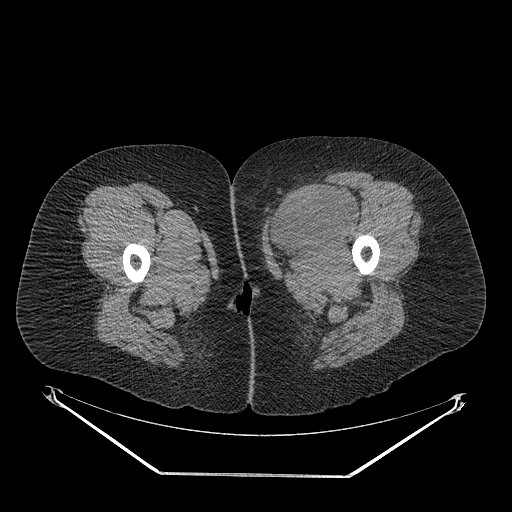
CT of an extremity soft-tissue mass (from a PET/CT study), one axial slice. Position 31 of 267 along the scan axis. Soft-tissue window (W 400 / L 40 HU). 3.75 mm slice thickness. 512 × 512 image matrix, field of view 500 × 500 mm. Female patient. From the clinical record (not read from this slice): histological type: myxofibrosarcoma; grade: intermediate; site of the primary tumour: left thigh.
Annotated regions visible in this slice (expert contour drawn on MRI and transferred to this co-registered scan by the dataset authors):
- gross tumour volume including surrounding oedema: box from (x=265, y=187) to (x=359, y=263) px
- gross tumour volume (mass): (x=267, y=187)–(x=355, y=248)